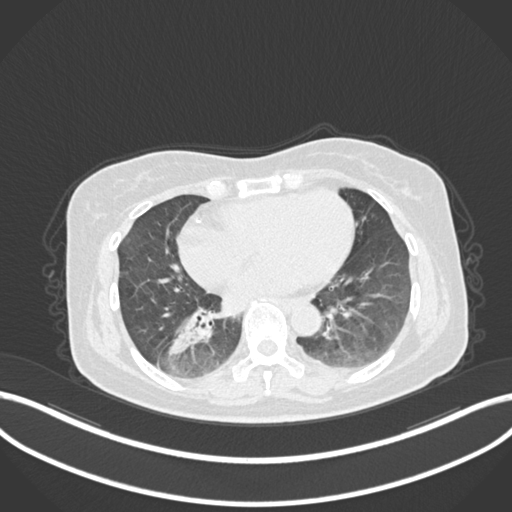
Chest CT, one axial slice; position 56 of 222 along the scan axis; reconstruction kernel B30f; 120 kVp; lung window (W 1500 / L -600 HU); 1 mm slice thickness; 512 × 512 image matrix, field of view 400 × 400 mm. Female patient, age 67 years. Case-level facts recorded for this patient, not image findings: clinical TNM (as recorded): T1c N1 M0.
Structures marked on this image (rectangle marked by the reading radiologist):
- lung tumour (recorded histology: adenocarcinoma): box from (x=163, y=301) to (x=222, y=369) px